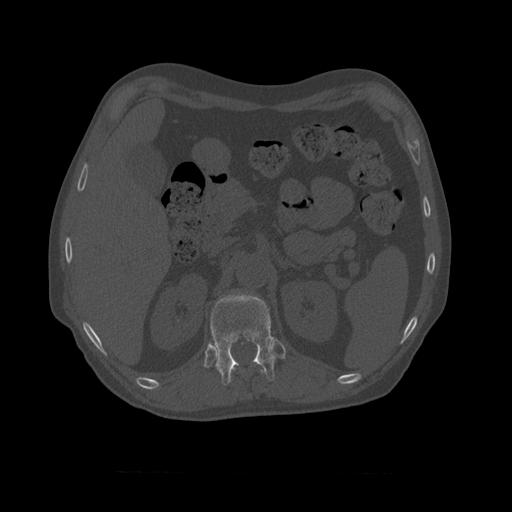
CT including the spine, one axial slice; position 381 of 450 along the scan axis; 120 kVp; bone window (W 1800 / L 400 HU); 1.25 mm slice thickness; 512 × 512 image matrix, field of view 405 × 405 mm. Patient age 75 years. Case-level facts recorded for this patient, not image findings: primary cancer: prostate.
Outlined on this slice (semi-automatically segmented with operator editing):
- T10 vertebra: bounding box <230,370,263,382> (left, top, right, bottom; pixels)
- T11 vertebra: <210,294,277,386>